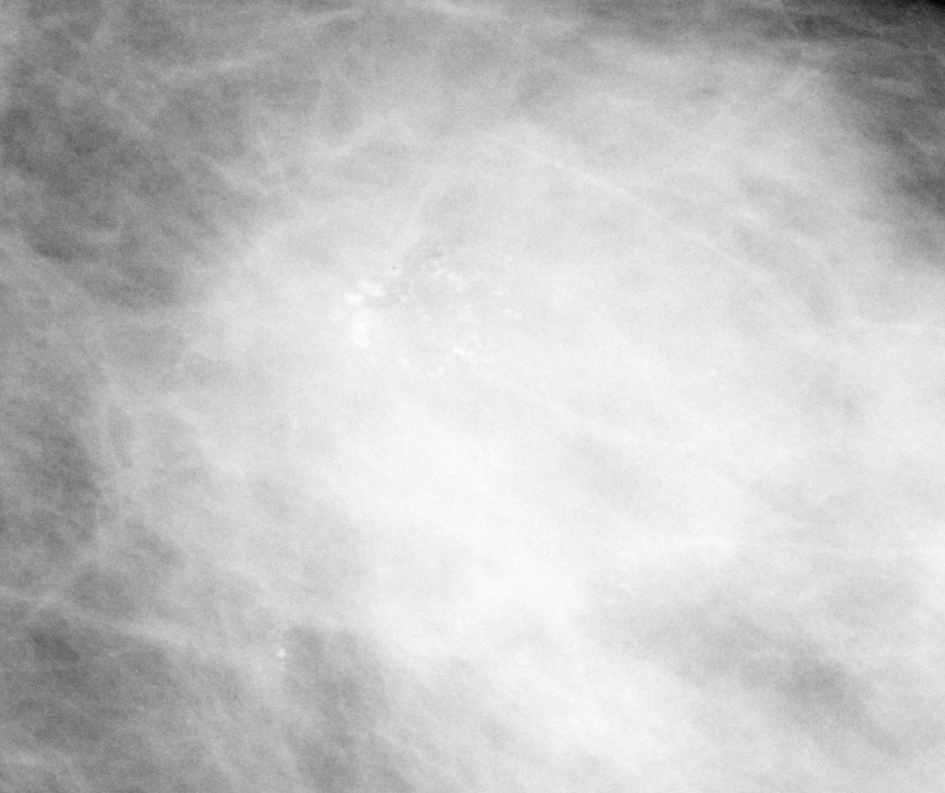
Cropped region of a digitized screen-film mammogram centred on a radiologist-marked abnormality; left breast; MLO view.
Marked abnormality: calcifications, morphology pleomorphic / fine linear branching, distribution regional; BI-RADS assessment category 5; subtlety rating 3 on a 1 (subtle) to 5 (obvious) scale; pathology result (as recorded, not read from the image): malignant.